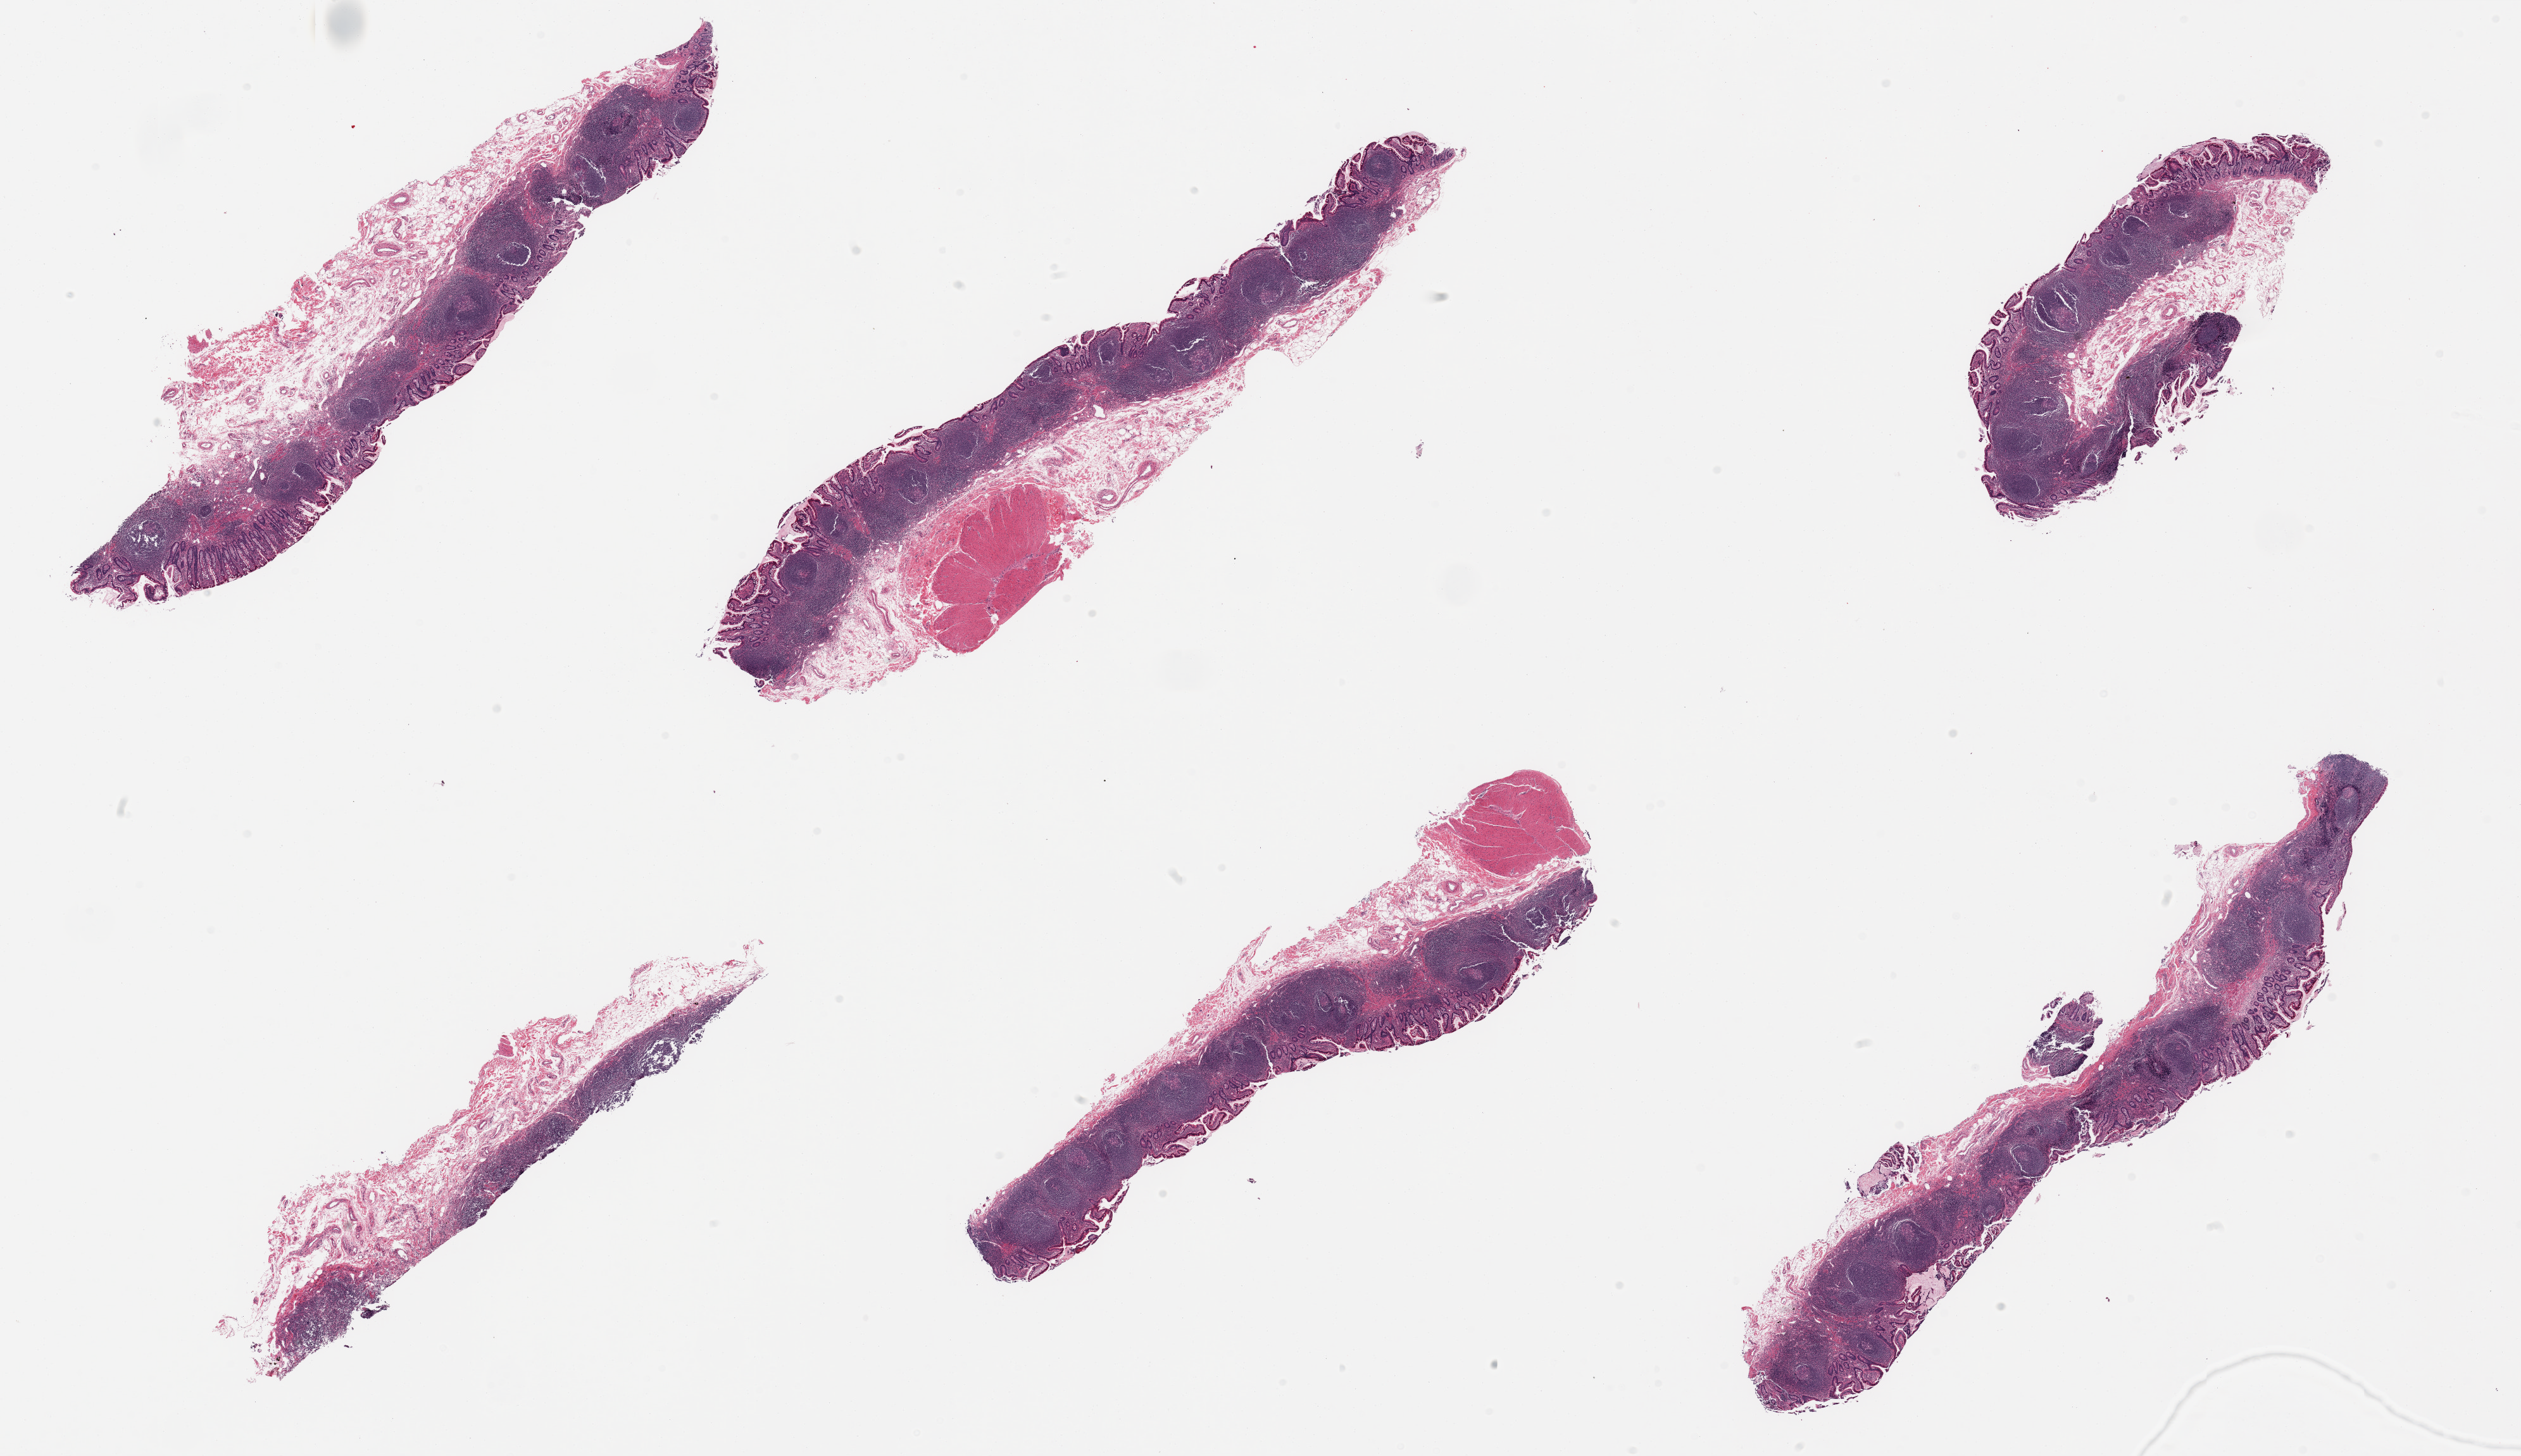
Digitized haematoxylin and eosin-stained section, a low-resolution overview of the entire scanned area, about 31.5 x 18.2 mm; PAXgene-fixed paraffin-embedded (PFPE) section; section of ileum (target tissue); donor tissue sample. Donor: male.
• reviewer comment on this tissue sample: 6 pieces; all have abundant lymphoid tissue; 2 have 1 and 2 mm extraneous muscularis propria